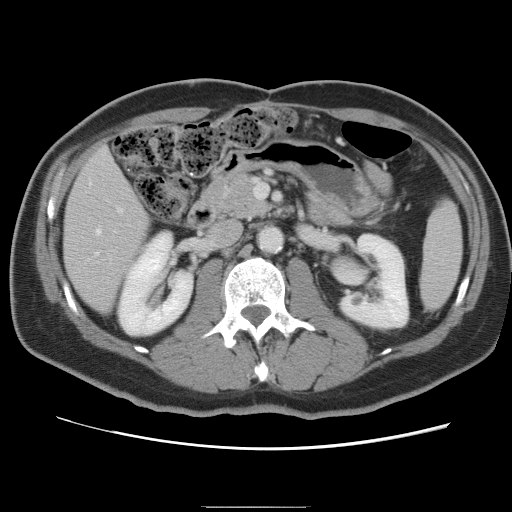
Contrast-enhanced abdominal CT, one axial slice; position 33 of 87 along the scan axis; 120 kVp; intravenous contrast given; soft-tissue window (W 400 / L 40 HU); 5 mm slice thickness; 512 × 512 image matrix. Male patient, age 63 years. Case-level facts recorded for this patient, not image findings: diagnosis: colorectal cancer liver metastases, imaged before liver resection.
Outlined on this slice (outlined manually by an expert reader):
- hepatic veins: bounding box [x1, y1, x2, y2] px = [96, 229, 101, 254]
- liver: [65, 149, 149, 312]
- planned liver remnant (the part of the liver to remain after resection): [65, 149, 151, 312]